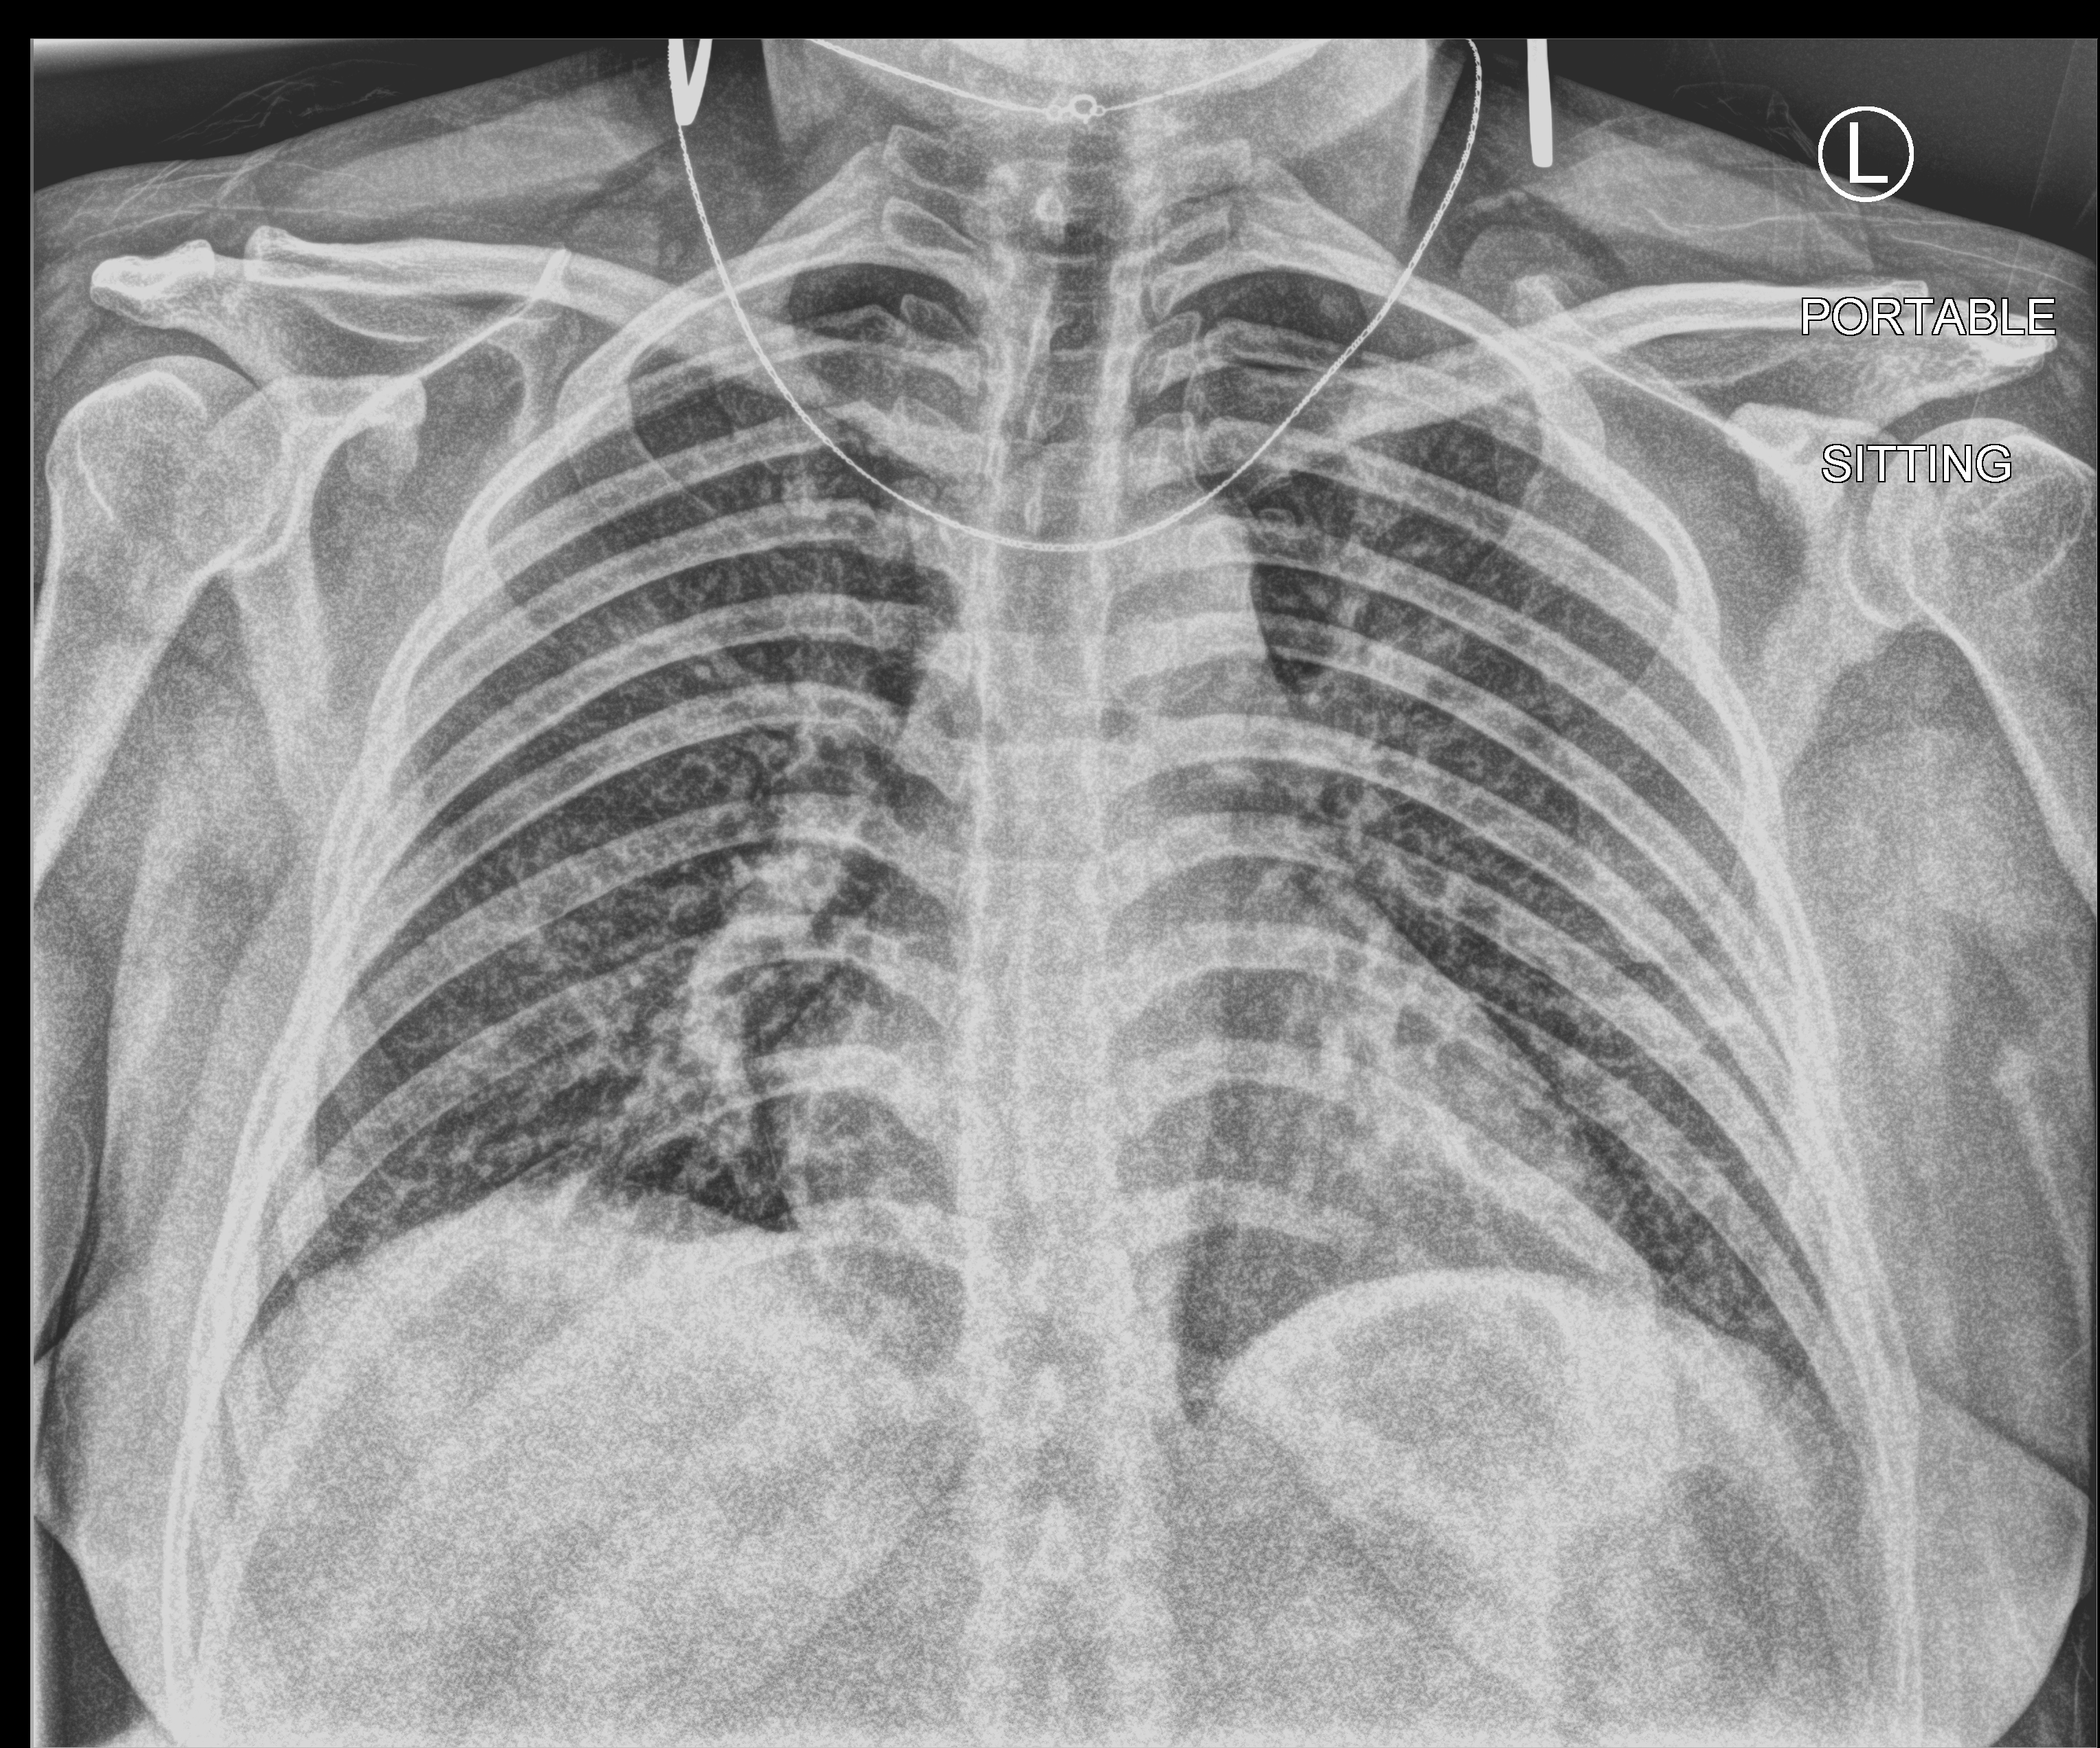
Bedside chest radiograph (computed radiography); anteroposterior (AP) projection. Patient hospitalised with COVID-19; female, aged 18–59 years.
Hospital-stay facts (about this admission, not read from this image; timing relative to this image not recorded): length of hospital stay: 1 day; admitted to intensive care during this hospital stay: no; mechanically ventilated during this hospital stay: no.